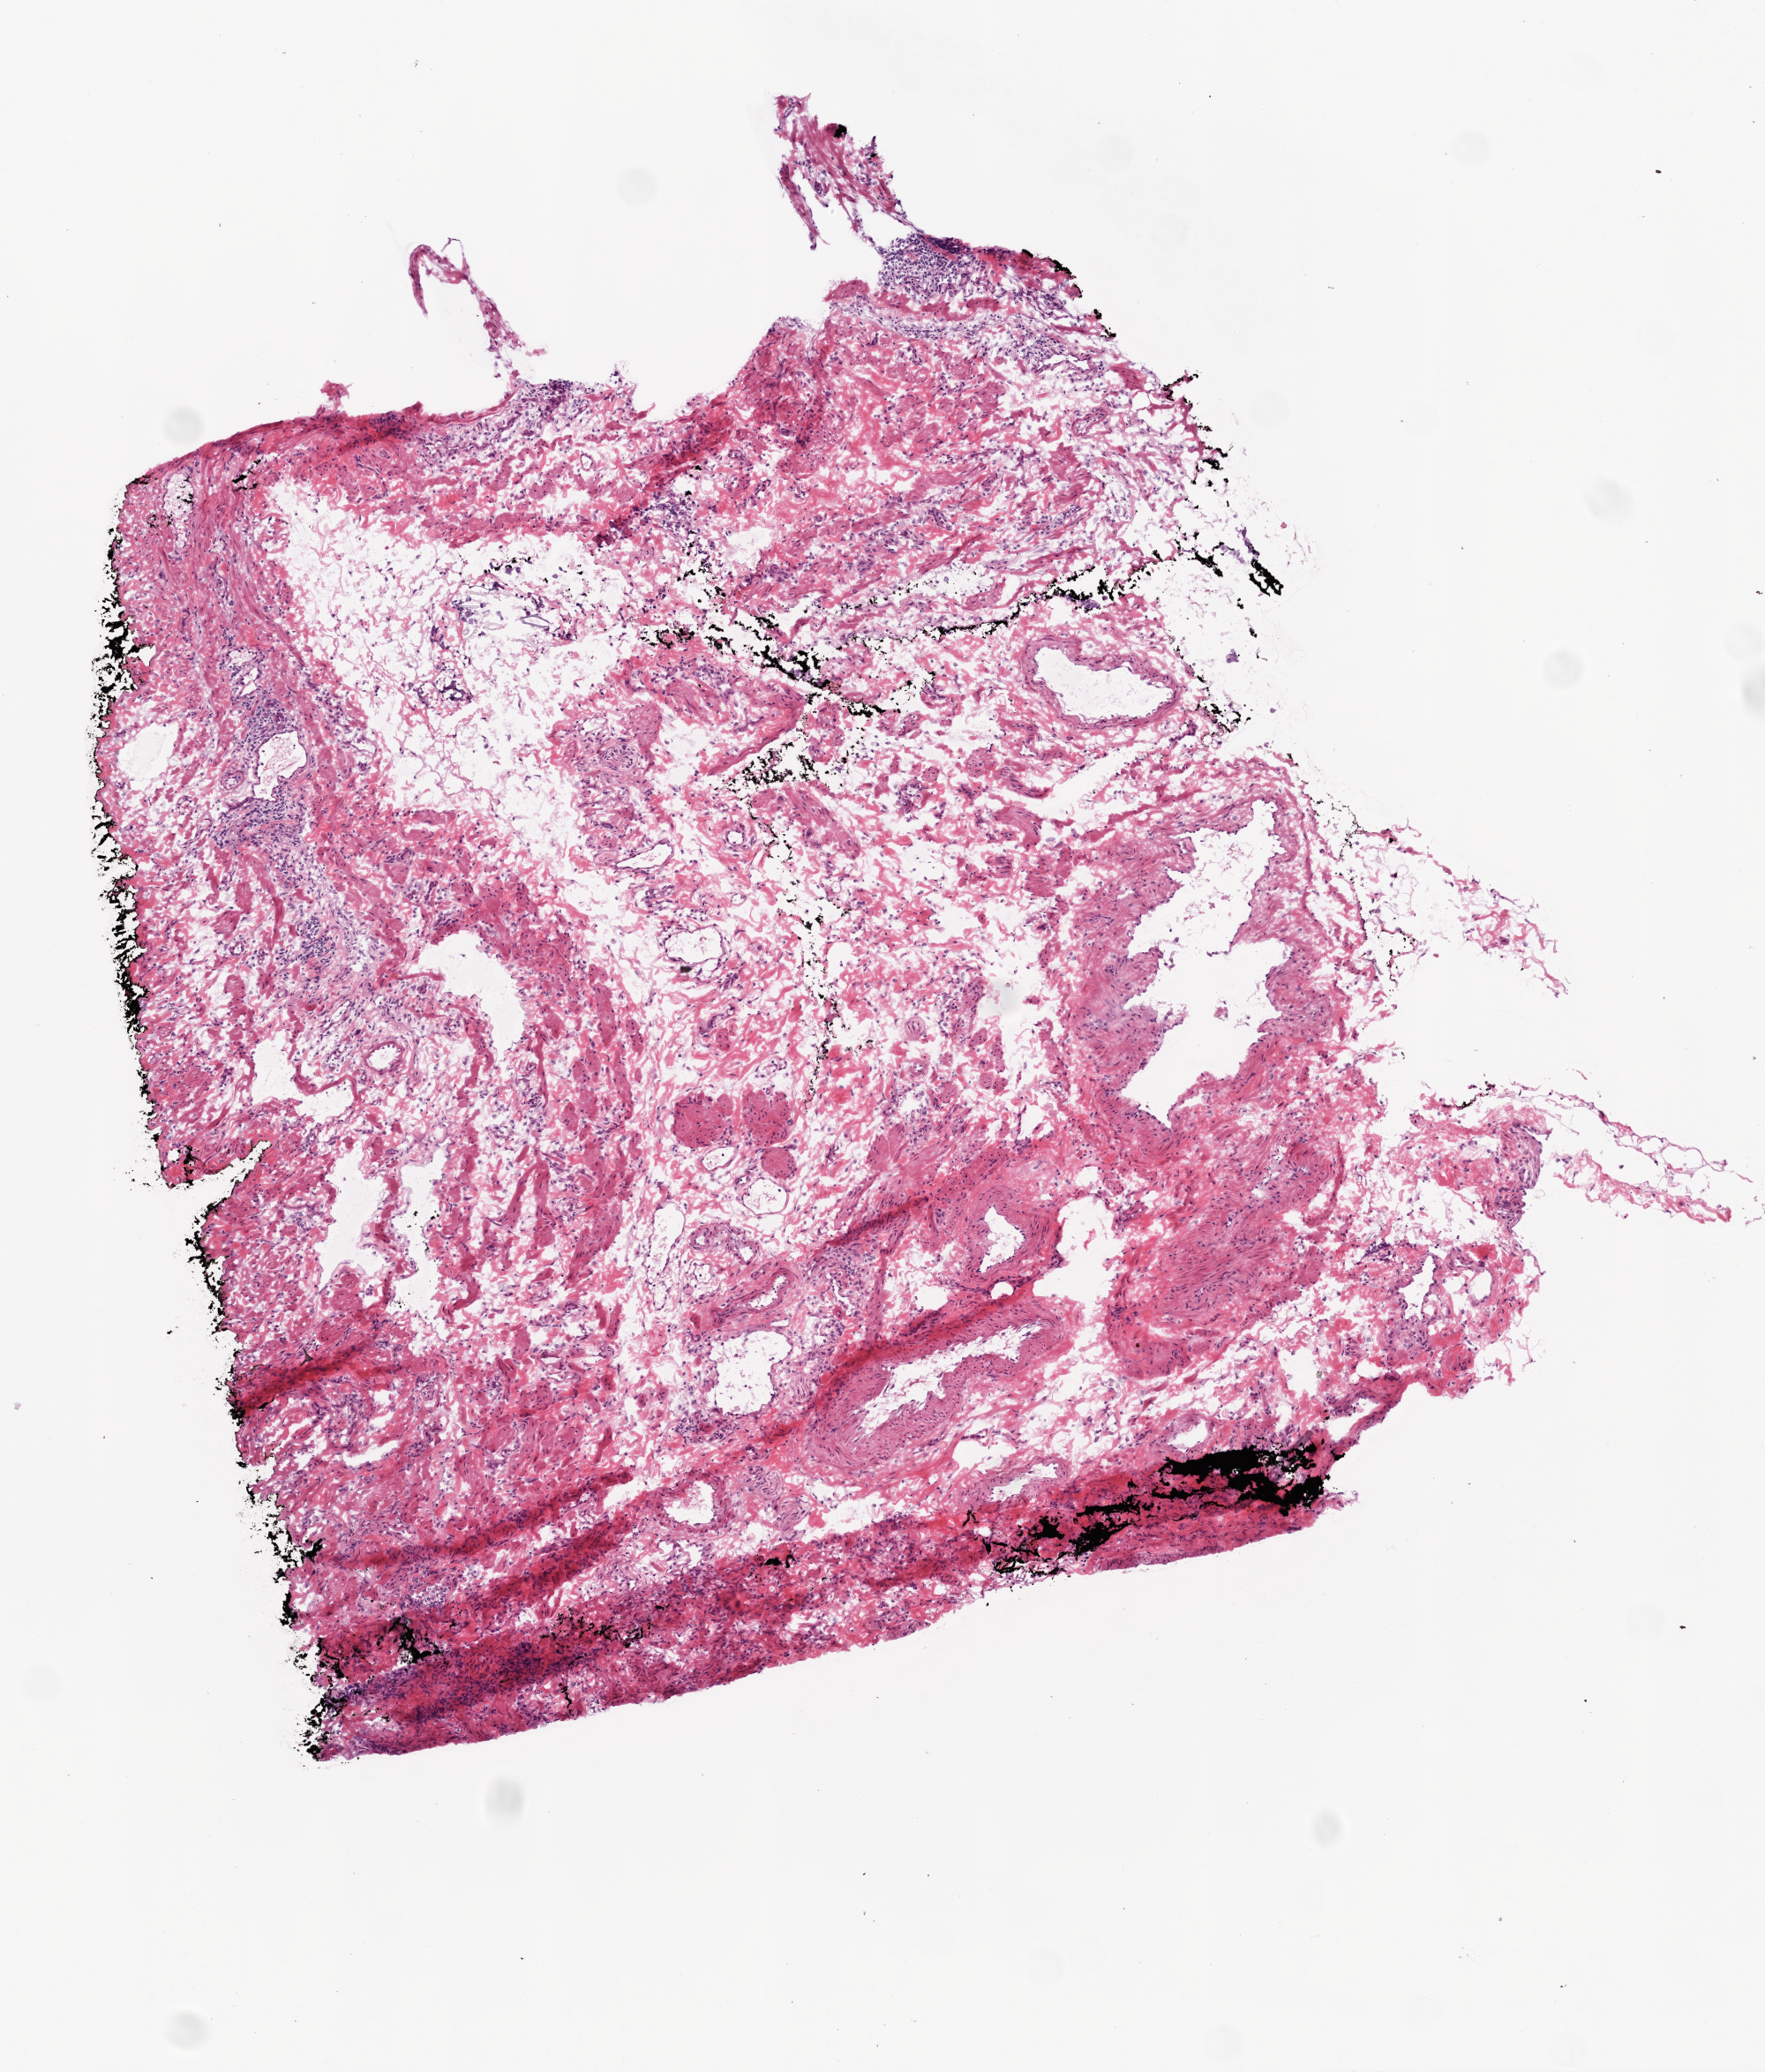
Whole-slide histology image, H&E, low-resolution overview of the scanned area, about 4.0 x 4.7 mm (slide scanned at 20x); frozen section from the top of the tissue portion; sample: solid tissue normal (non-tumour tissue), ovary. Patient: female, age at initial diagnosis 57 years.
This section: solid tissue normal (non-tumour) sample from the same patient. Patient diagnosis: Serous cystadenocarcinoma, NOS.